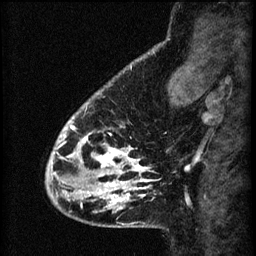
Breast MRI (dynamic contrast-enhanced), one sagittal slice; slice 14 of 60 in the series (ordered by position); 3 images stored at this slice position (order not interpretable as contrast timing); 1.5 T; TE 4.2 ms, TR 8.2 ms; 2.2 mm slice thickness; 256 × 256 image matrix. Female patient, age 41 years.
Structures marked on this image (semi-automatic segmentation, software-assisted and operator-edited):
- analysis volume of interest (the breast-tissue region the enhancement analysis was run in; not a lesion): bounding box <56,104,156,207> (left, top, right, bottom; pixels)
- tumour enhancement mask (voxels above the 70 % enhancement threshold inside the analysis volume of interest): <56,104,153,207>